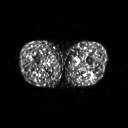
FDG PET of an extremity soft-tissue mass (from a PET/CT study), one axial slice; slice 228 of 267 in the series (ordered by position); 3.27 mm slice thickness; 128 × 128 image matrix, field of view 500 × 500 mm. Patient: male, 27 years. From the clinical record (not read from this slice): histological type: extraskeletal osteosarcoma; grade: high; site of the primary tumour: left adductur.
Structures marked on this image (expert contour drawn on MRI and transferred to this co-registered scan by the dataset authors):
- gross tumour volume (mass): bounding box (x1, y1, x2, y2) in pixels: (68, 61, 92, 78)